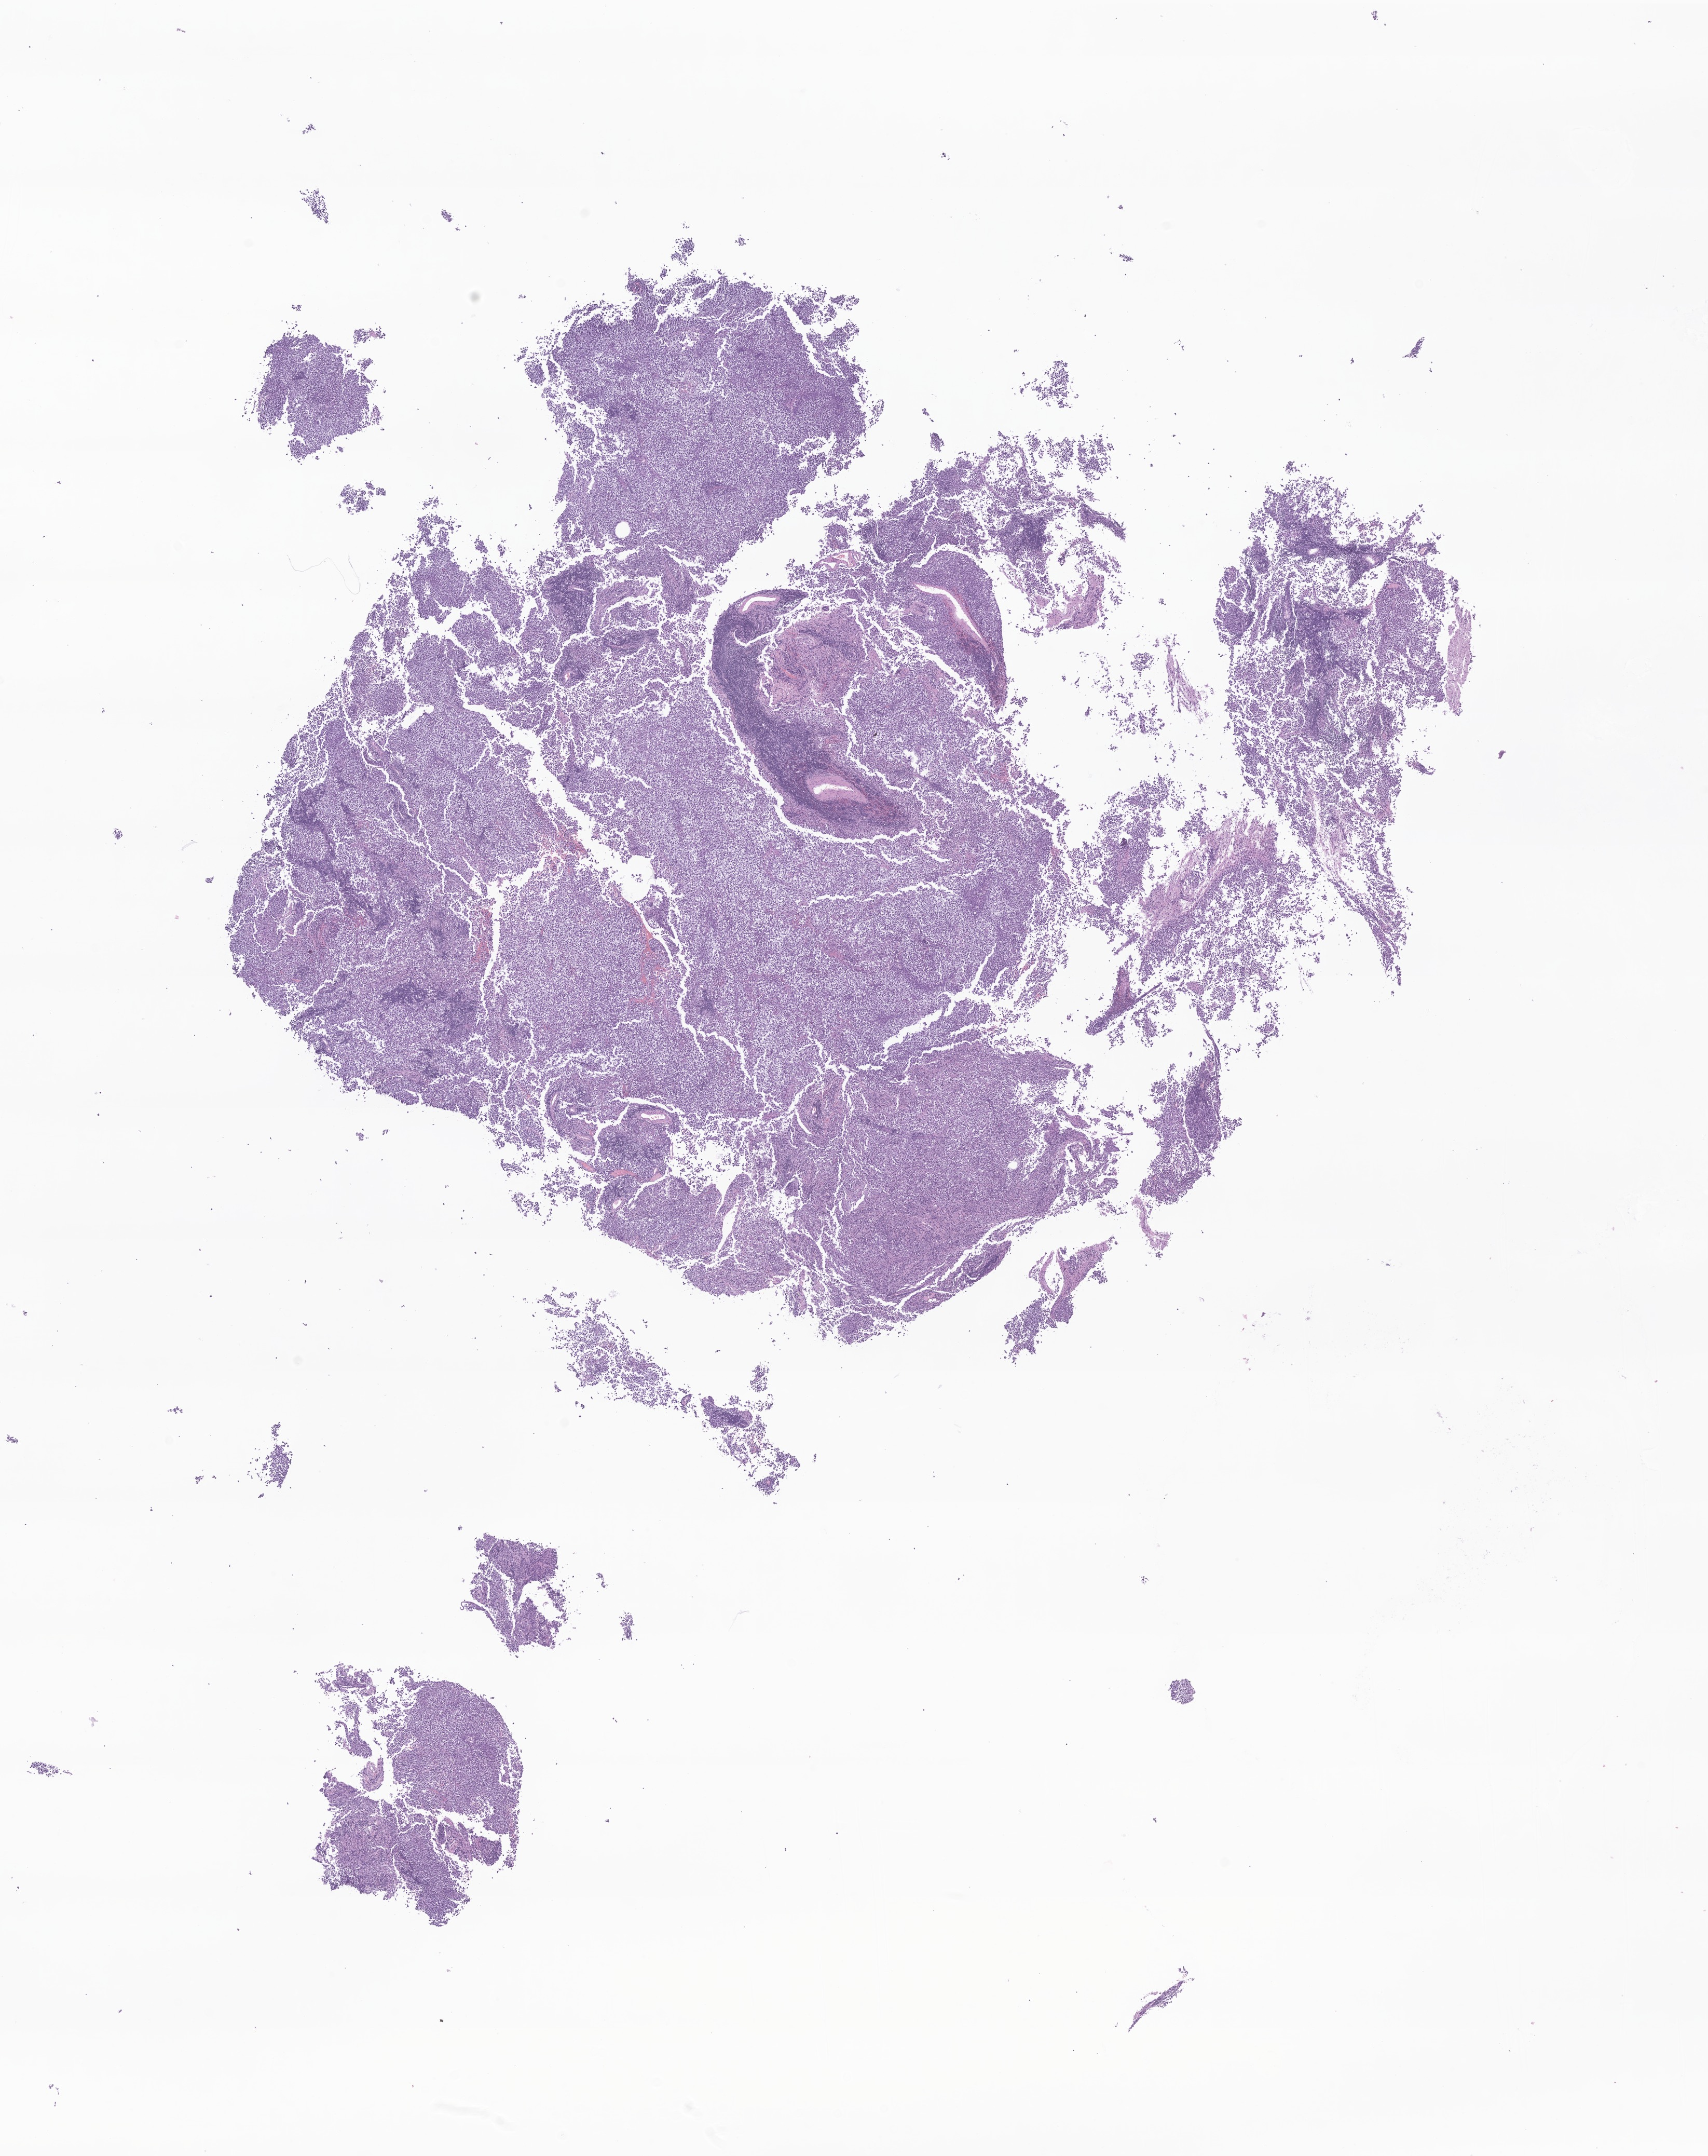
H&E whole-slide image of tumor tissue from the frontal lobe — a low-resolution overview of the entire scanned area, about 13.9 x 17.5 mm, FFPE section. Patient: female, age 100 months (8 years 4 months).
Diagnosis (ICD-O-3 morphology term): Neoplasm, uncertain whether benign or malignant.